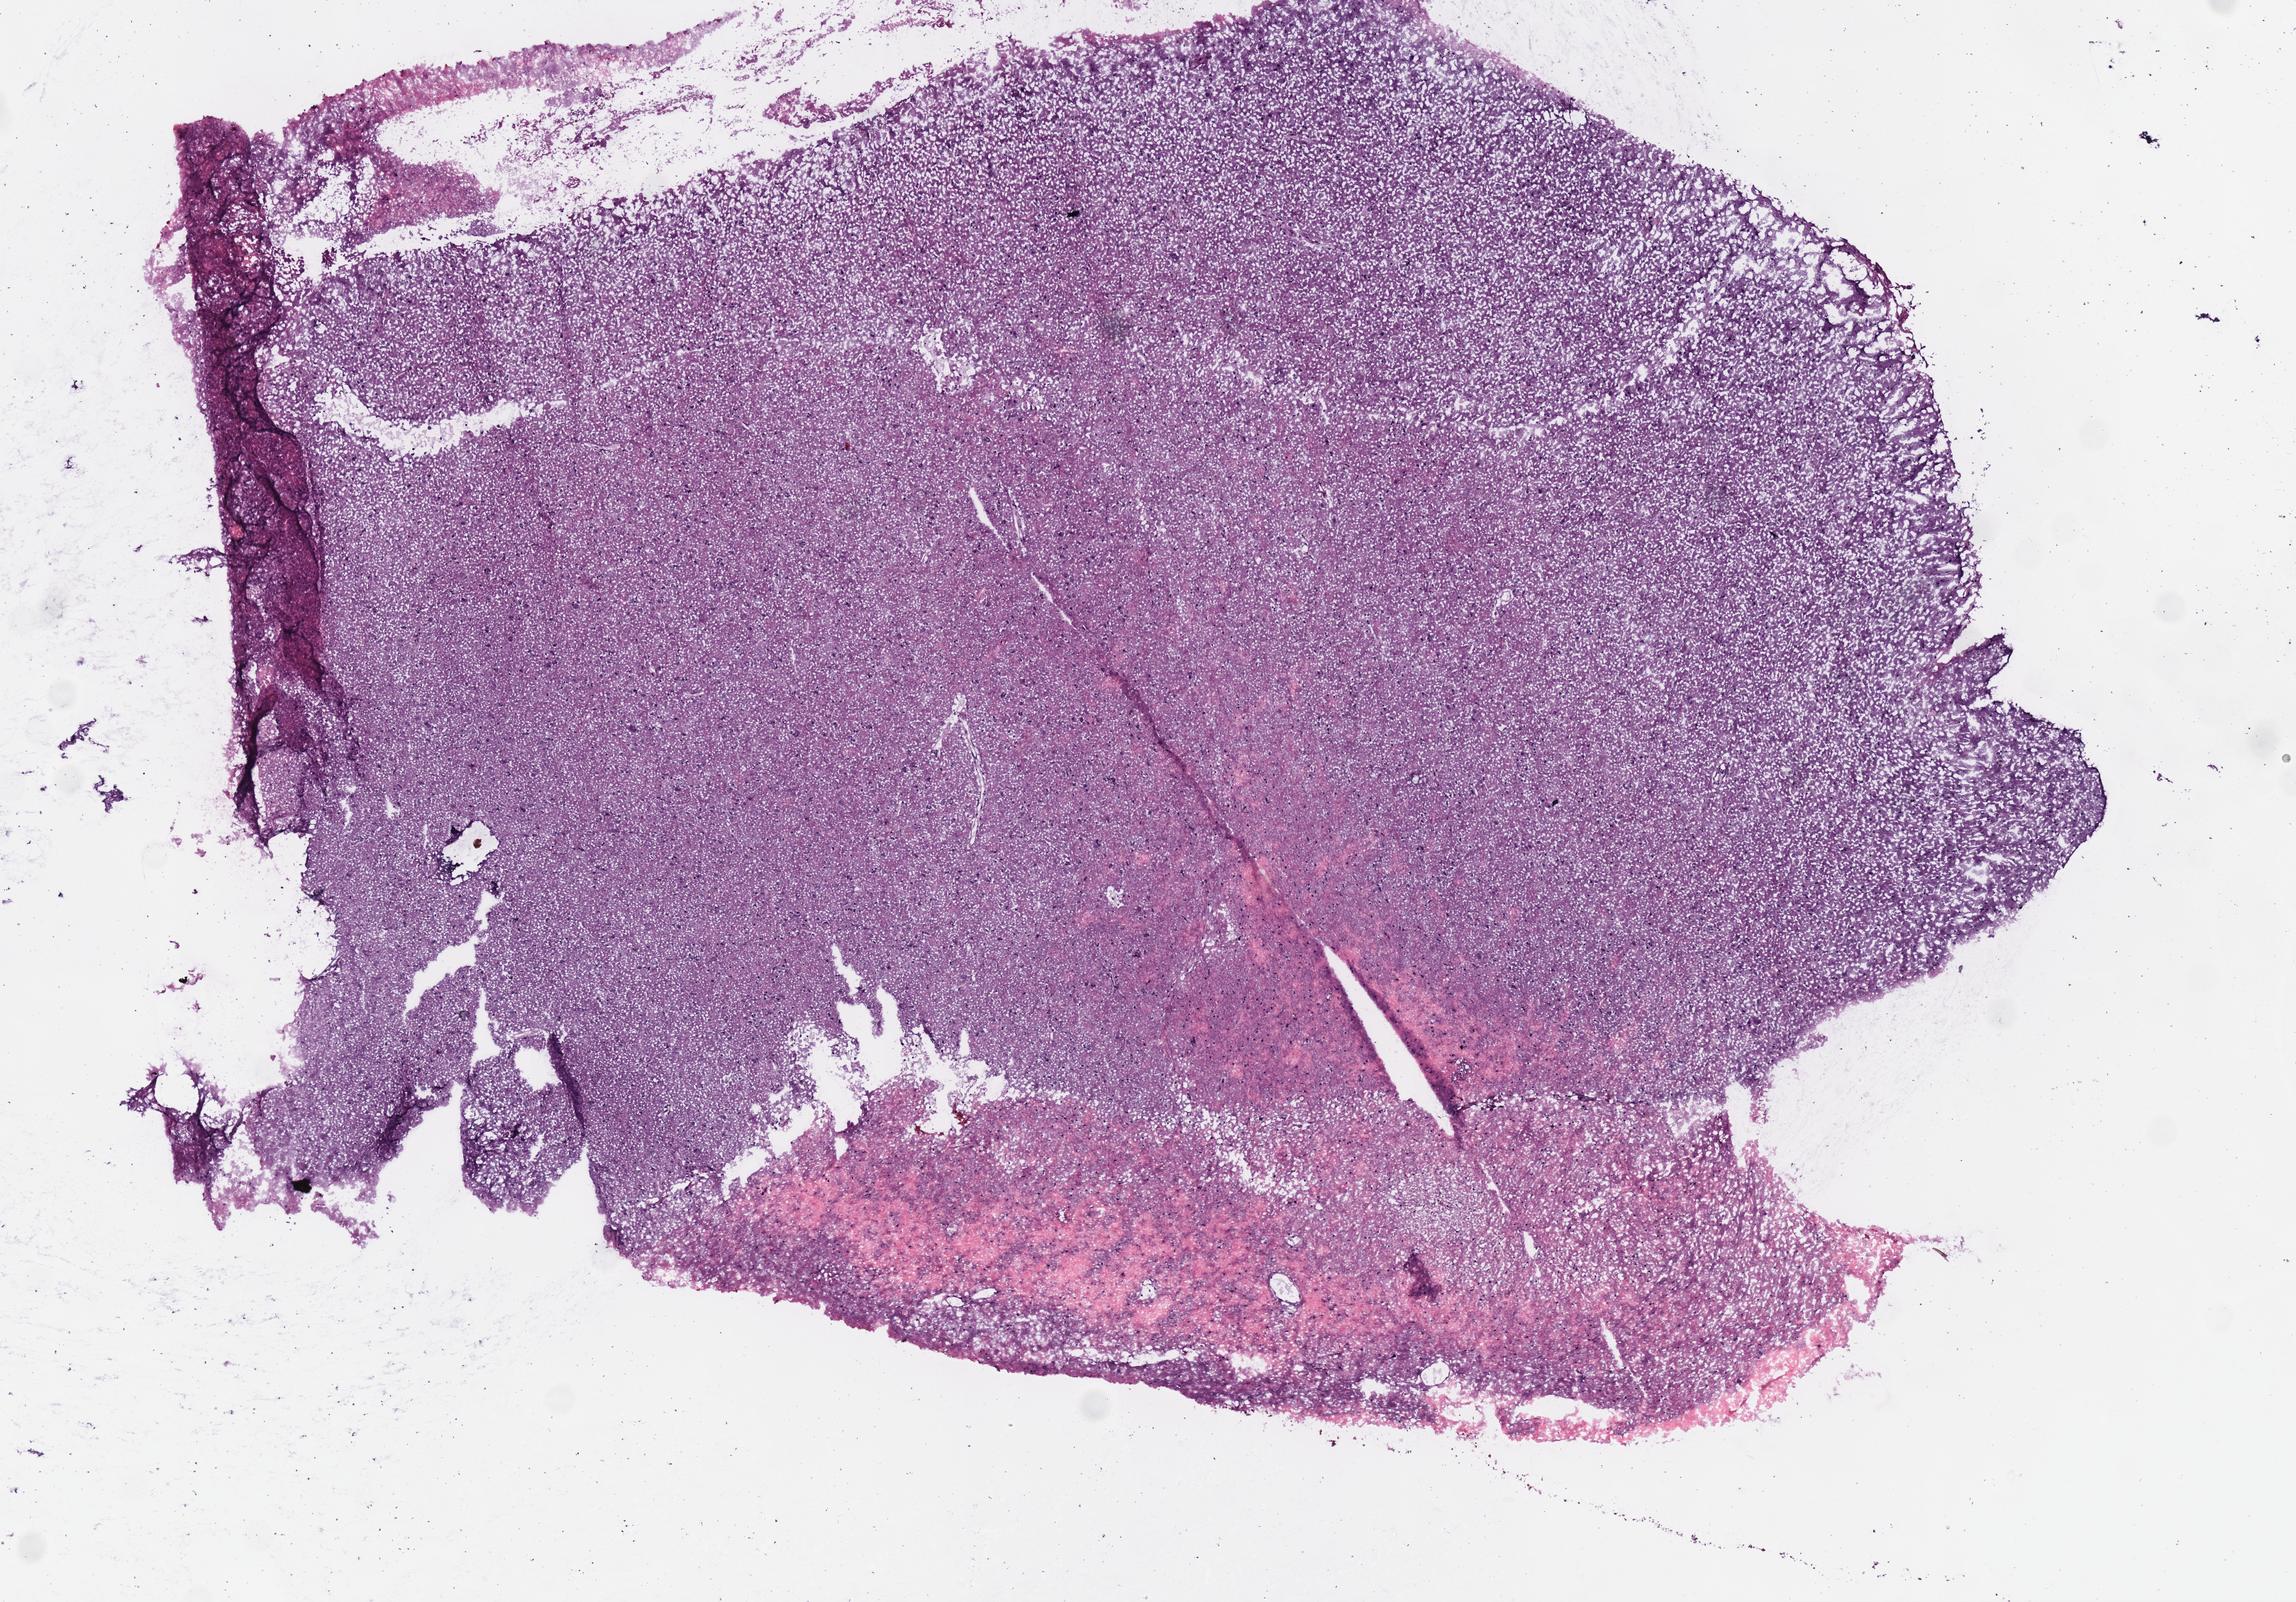
H&E-stained whole-slide image, a low-resolution overview of the entire scanned area, about 6.4 x 4.4 mm; frozen section from the top of the tissue portion; brain, primary tumour sample. Male patient; age at initial diagnosis 62 years. Histologic grade: G2 (moderately differentiated). Composition of this section per pathologist review: tumour cells 100%, tumour nuclei 60%, normal cells 0%, stromal cells 0%, necrosis 0%.
Histologic diagnosis: Oligodendroglioma, NOS.